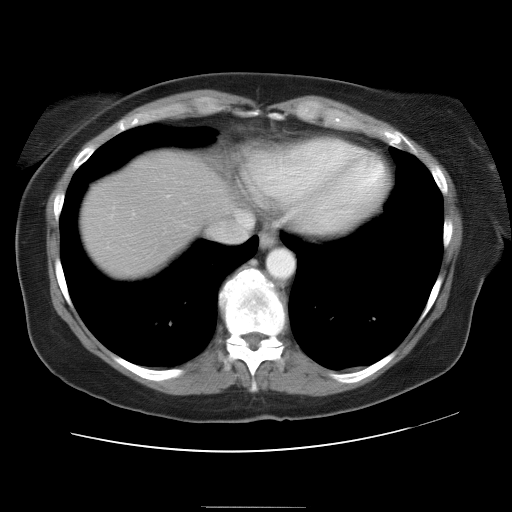
Contrast-enhanced abdominal CT, one axial slice; reconstruction kernel STANDARD; intravenous contrast given; soft-tissue window (W 400 / L 40 HU); 7.5 mm slice thickness; 512 × 512 image matrix, field of view 376 × 376 mm. Female patient, age 52 years. Case-level facts recorded for this patient, not image findings: diagnosis: colorectal cancer liver metastases, imaged before liver resection; multiple liver metastases: no; largest metastasis: 3 cm; chemotherapy before resection: yes.
Structures marked on this image (outlined manually by an expert reader):
- liver: bounding box [x1, y1, x2, y2] px = [80, 152, 231, 278]
- planned liver remnant (the part of the liver to remain after resection): [194, 161, 231, 199]